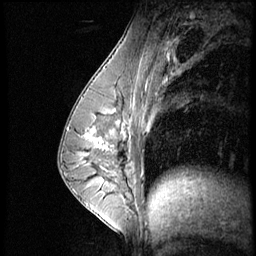
Breast MRI (dynamic contrast-enhanced), one sagittal slice; slice 29 of 56 in the series (ordered by position); dynamic contrast-enhanced series, image 2 of 4 at this slice position (ordered by acquisition); 1.5 T; TE 4.2 ms, TR 8.9 ms; 2.5 mm slice thickness; 256 × 256 image matrix, field of view 200 × 200 mm. Female patient, age 35 years. From the clinical record (not read from this slice): setting: breast cancer imaged before/during neoadjuvant chemotherapy; receptor status: HER2-positive.
Annotated regions visible in this slice (semi-automatically segmented with operator editing):
- analysis volume of interest (the breast-tissue region the enhancement analysis was run in; not a lesion): bounding box <73,111,131,164> (left, top, right, bottom; pixels)
- tumour enhancement mask (voxels above the 140 % enhancement threshold inside the analysis volume of interest): <85,129,115,149>